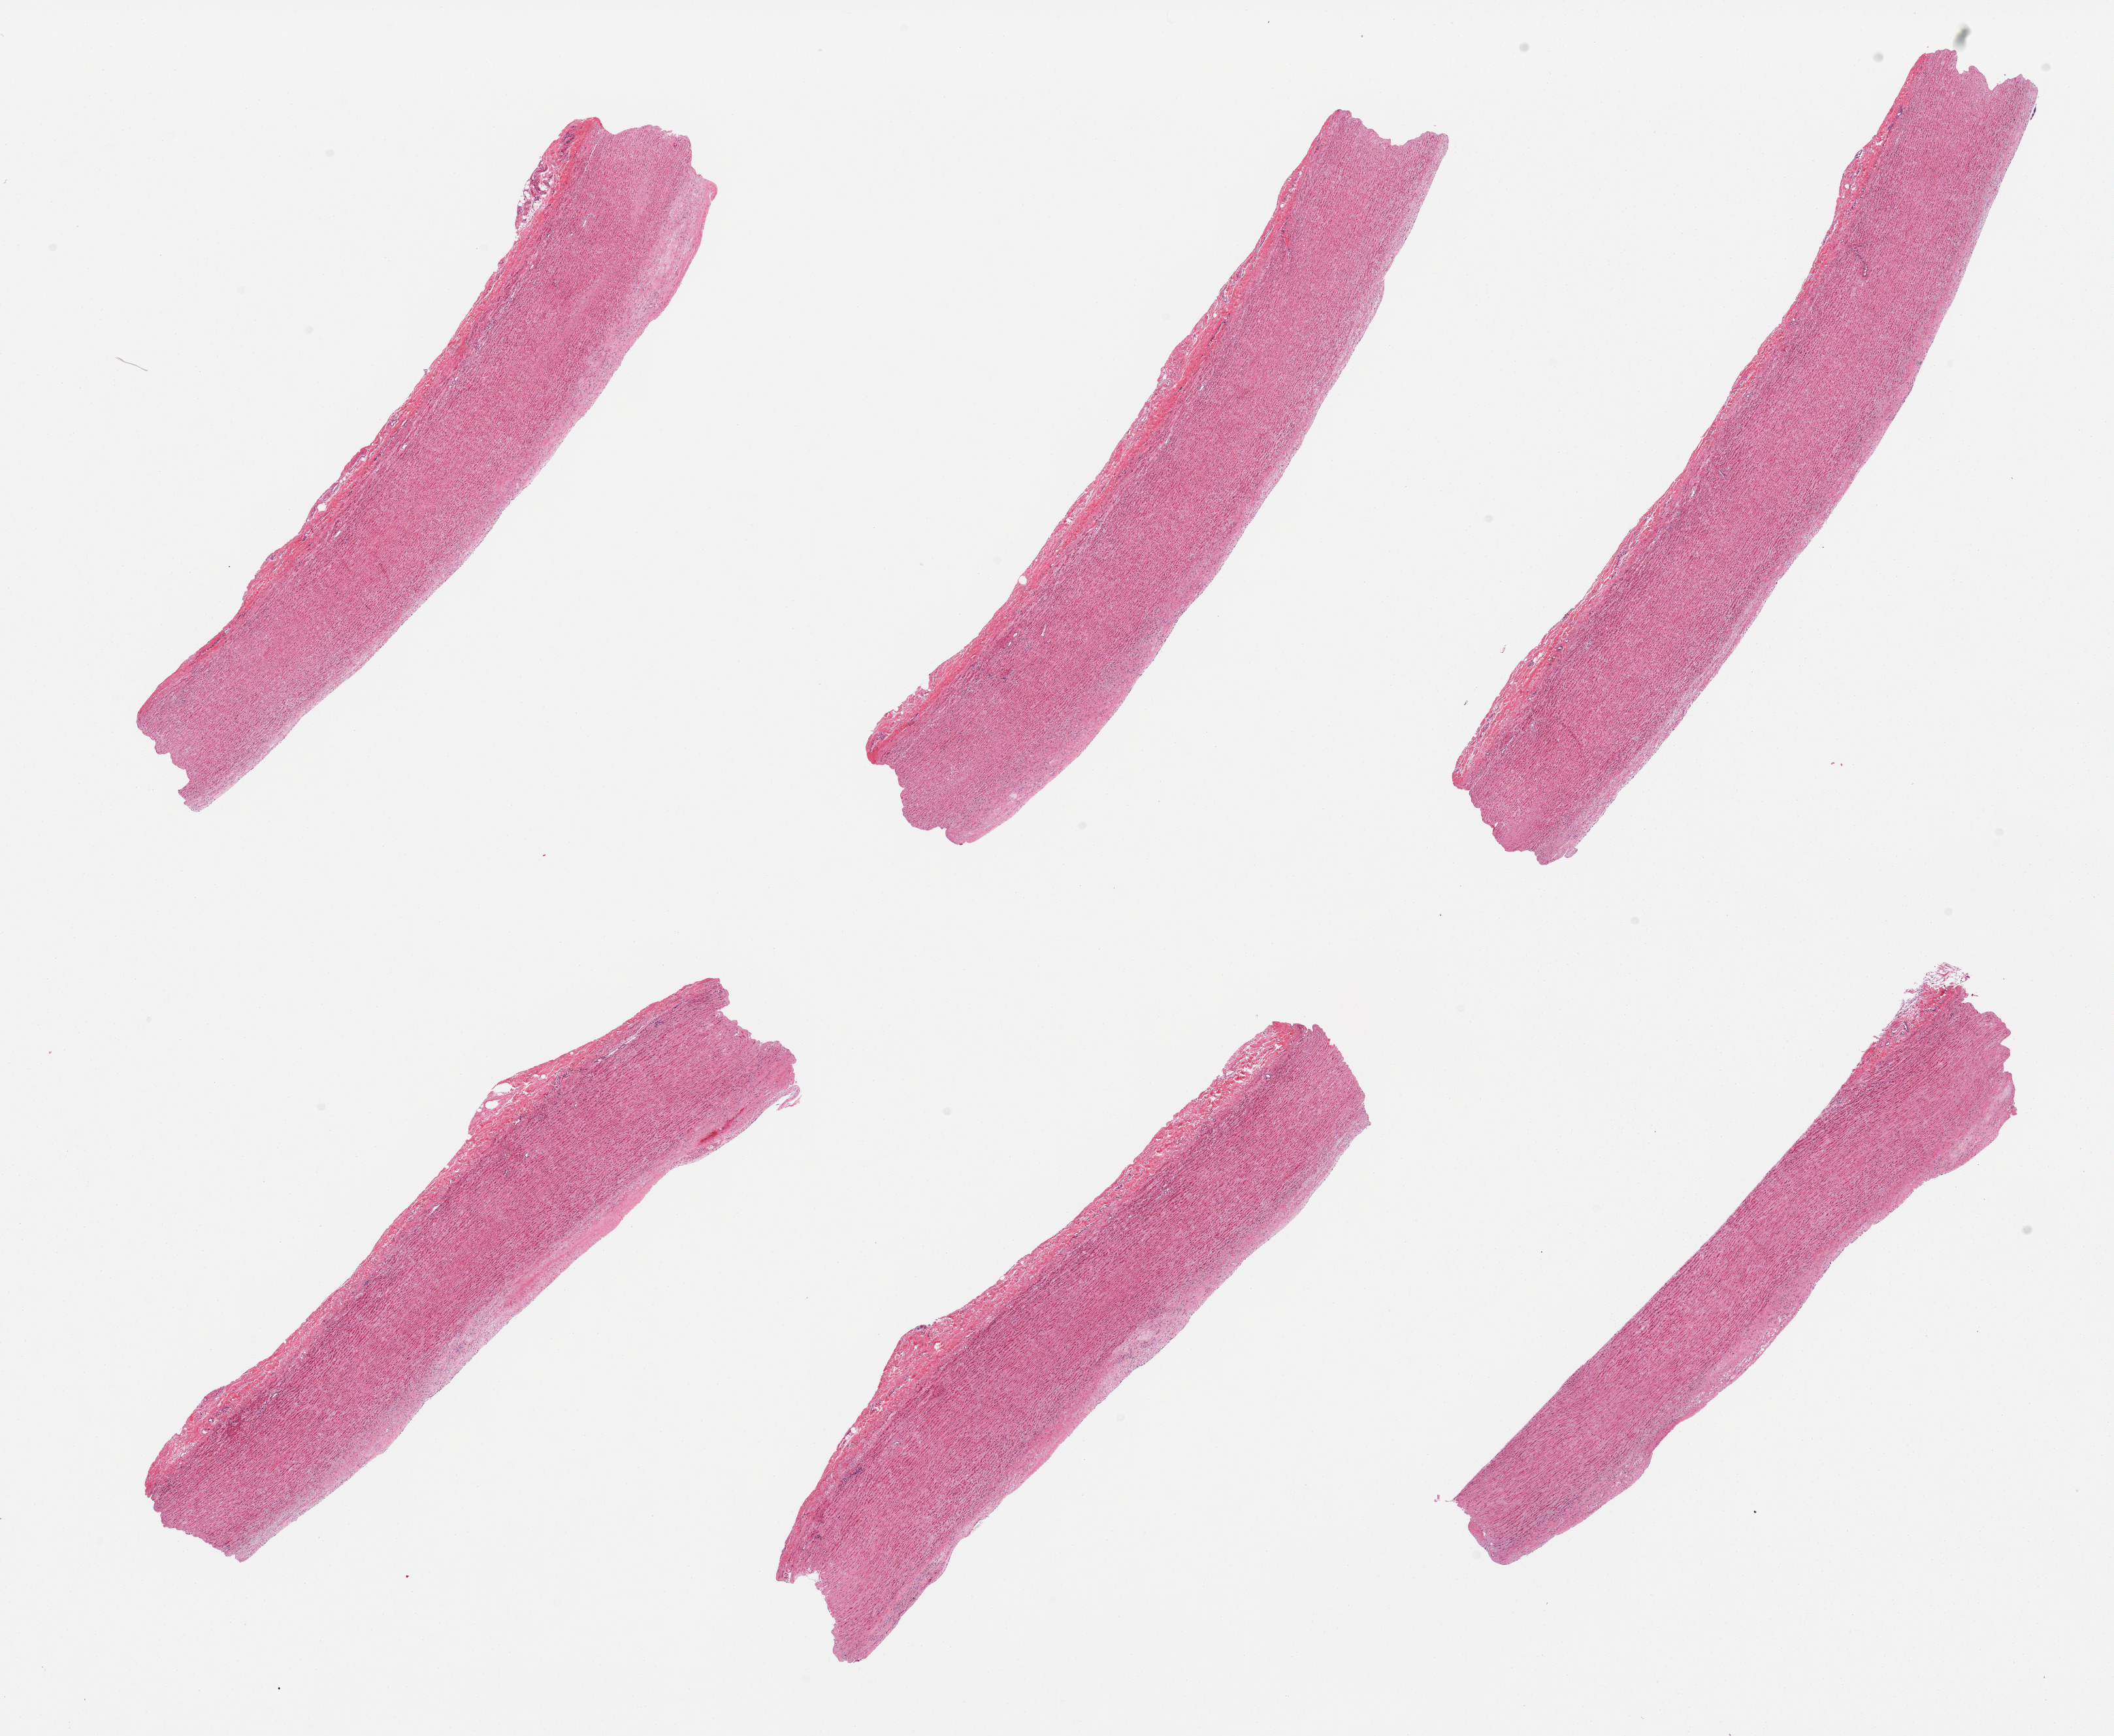
Digitized hematoxylin and eosin (H&E)-stained section — a low-resolution overview of the entire scanned area, about 25.6 x 21.0 mm (acquisition: 20x scan). PAXgene-fixed paraffin-embedded (PFPE) section. Target tissue: aorta. Donor tissue sample. Donor: female.
* reviewer comment on this tissue sample: 6 pieces, minimal atherosis